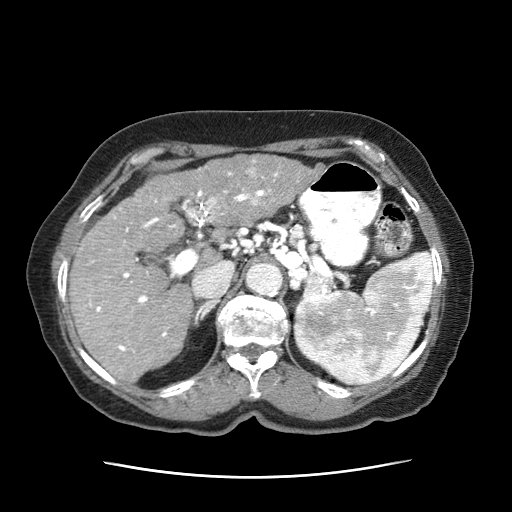
Contrast-enhanced abdominal CT (liver protocol), one axial slice; slice 37 of 63 in the series (ordered by position); 120 kVp; intravenous contrast given; soft-tissue window (W 400 / L 40 HU); 2.5 mm slice thickness; 512 × 512 image matrix, field of view 360 × 360 mm. Female patient, age 79 years. Case-level facts recorded for this patient, not image findings: diagnosis: hepatocellular carcinoma (patient treated with transarterial chemoembolisation; whether this scan precedes or follows treatment is not stated here); TNM stage (as recorded): Stage-II; Child-Pugh class: B; tumour differentiation: well differentiated; tumour nodularity: multinodular.
Annotated regions visible in this slice (semi-automatic segmentation, software-assisted and operator-edited):
- abdominal aorta: bounding box (x1, y1, x2, y2) in pixels: (246, 263, 282, 296)
- liver parenchyma outside the tumour (the mass and vessels are separate outlines, so this box may not span the whole liver): (69, 176, 236, 383)
- mass: (153, 154, 321, 223)
- liver vessels: (86, 172, 278, 353)